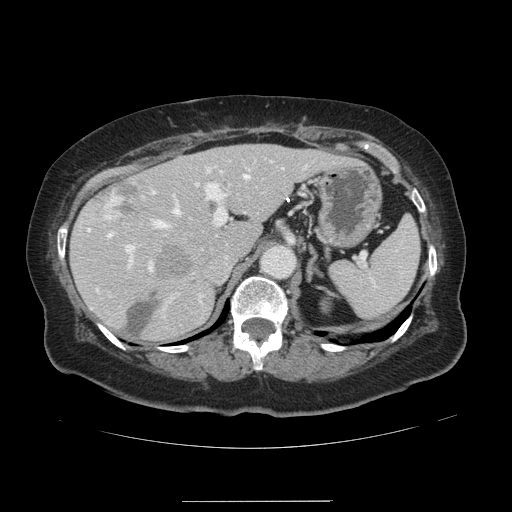
Contrast-enhanced abdominal CT, one axial slice; slice 86 of 141 in the series (ordered by position); intravenous contrast given; soft-tissue window (W 400 / L 40 HU); 2.5 mm slice thickness; 512 × 512 image matrix, field of view 393 × 393 mm. Female patient, age 74 years. From the clinical record (not read from this slice): diagnosis: colorectal cancer liver metastases, imaged before liver resection; multiple liver metastases: yes; largest metastasis: 7 cm; disease in both lobes: yes.
Outlined on this slice (expert manual segmentation):
- hepatic veins: box from (x=108, y=175) to (x=248, y=298) px
- liver: (x=72, y=145)–(x=340, y=341)
- planned liver remnant (the part of the liver to remain after resection): (x=72, y=145)–(x=340, y=341)
- portal vein (with intrahepatic branches): (x=125, y=166)–(x=306, y=269)
- liver metastasis: (x=96, y=179)–(x=157, y=226)
- liver metastasis: (x=127, y=293)–(x=159, y=334)
- liver metastasis: (x=157, y=245)–(x=192, y=277)